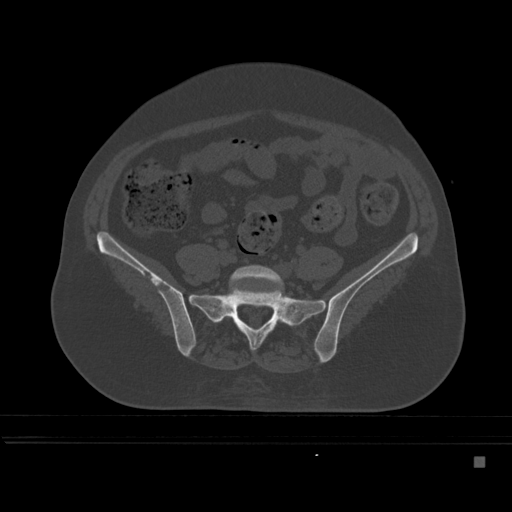
CT including the spine, one axial slice; bone window (W 1800 / L 400 HU); 1.5 mm slice thickness; 512 × 512 image matrix, field of view 404 × 404 mm. Patient: female, 33 years. Case-level facts recorded for this patient, not image findings: primary cancer: breast.
Annotated regions visible in this slice (semi-automatic segmentation, software-assisted and operator-edited):
- L5 vertebra: bounding box <222,265,284,320> (left, top, right, bottom; pixels)